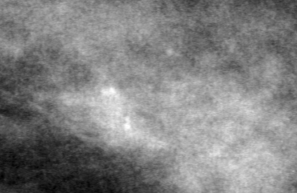
Region of interest cut from a scanned film mammogram (one marked finding); right breast; CC view.
Marked abnormality: calcifications, morphology pleomorphic, distribution clustered; BI-RADS assessment category 4; subtlety rating 2 on a 1 (subtle) to 5 (obvious) scale; pathology (as recorded): benign.